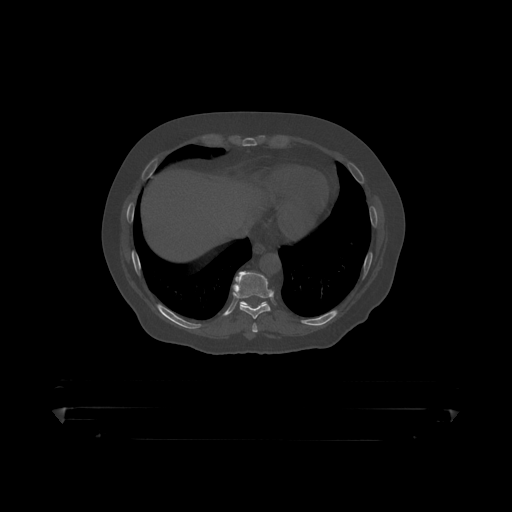
CT including the spine, one axial slice; slice 234 of 390 in the series (ordered by position); reconstruction kernel STANDARD; 120 kVp; bone window (W 1800 / L 400 HU); 1.25 mm slice thickness; 512 × 512 image matrix, field of view 650 × 650 mm. Male patient, age 60 years. Case-level facts recorded for this patient, not image findings: primary cancer: prostate.
Outlined on this slice (semi-automatically segmented with operator editing):
- T10 vertebra: box from (x=240, y=301) to (x=266, y=307) px
- T9 vertebra: (x=232, y=271)–(x=272, y=319)